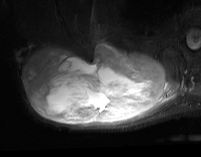
MRI of an extremity soft-tissue mass, one axial slice; position 38 of 74 along the scan axis; STIR; MR volume resampled by the dataset authors to the PET/CT grid (not the native acquisition matrix); 3.27 mm slice thickness; 201 × 157 image matrix, field of view 196 × 153 mm. Male patient. Case-level facts recorded for this patient, not image findings: histological type: pleiomorphic spindle cell undifferentiated; grade: high; site of the primary tumour: right parascapusular.
Annotated regions visible in this slice (expert contour drawn on MRI and transferred to this co-registered scan by the dataset authors):
- gross tumour volume including surrounding oedema: box from (x=24, y=41) to (x=180, y=126) px
- gross tumour volume (mass): (x=24, y=43)–(x=166, y=126)